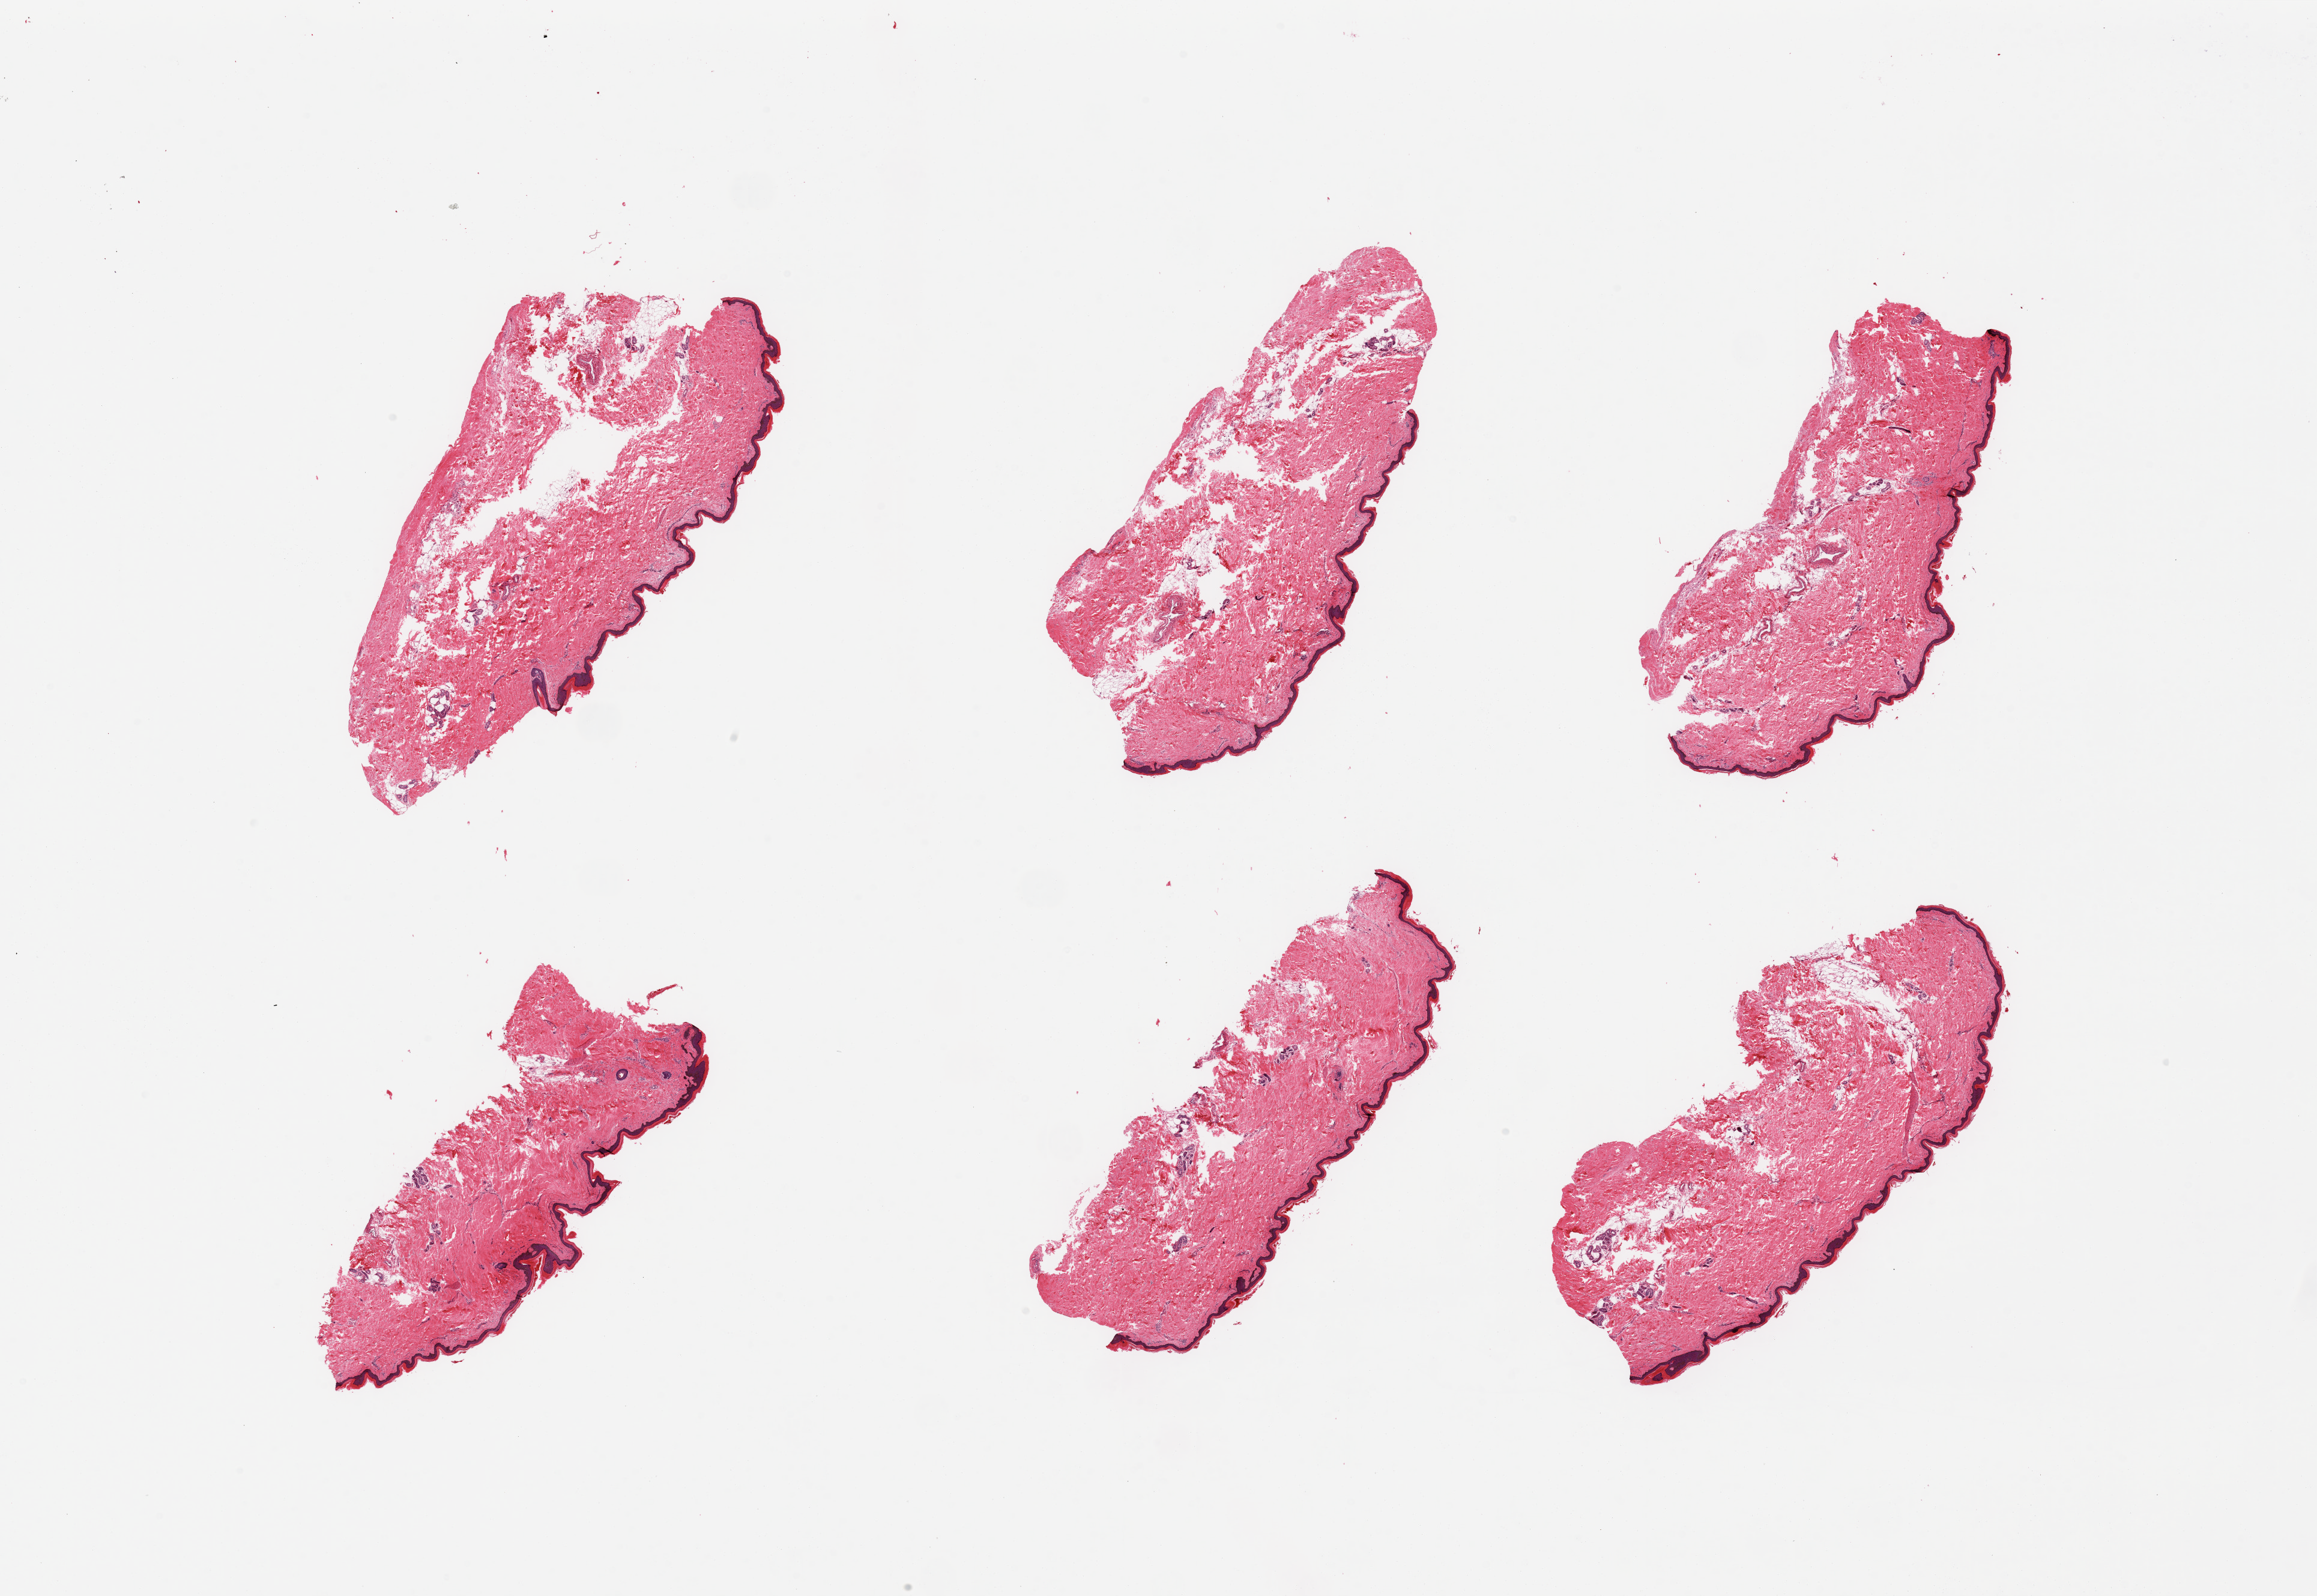
Digitized haematoxylin and eosin-stained section, low-resolution overview of the scanned area, about 30.5 x 21.0 mm; PAXgene-fixed paraffin-embedded (PFPE) section; section of skin of lower leg (target tissue); donor tissue sample. Donor: female.
Review note (as recorded): 6 pieces; ~10% internal fat, but multiple tissue defects.